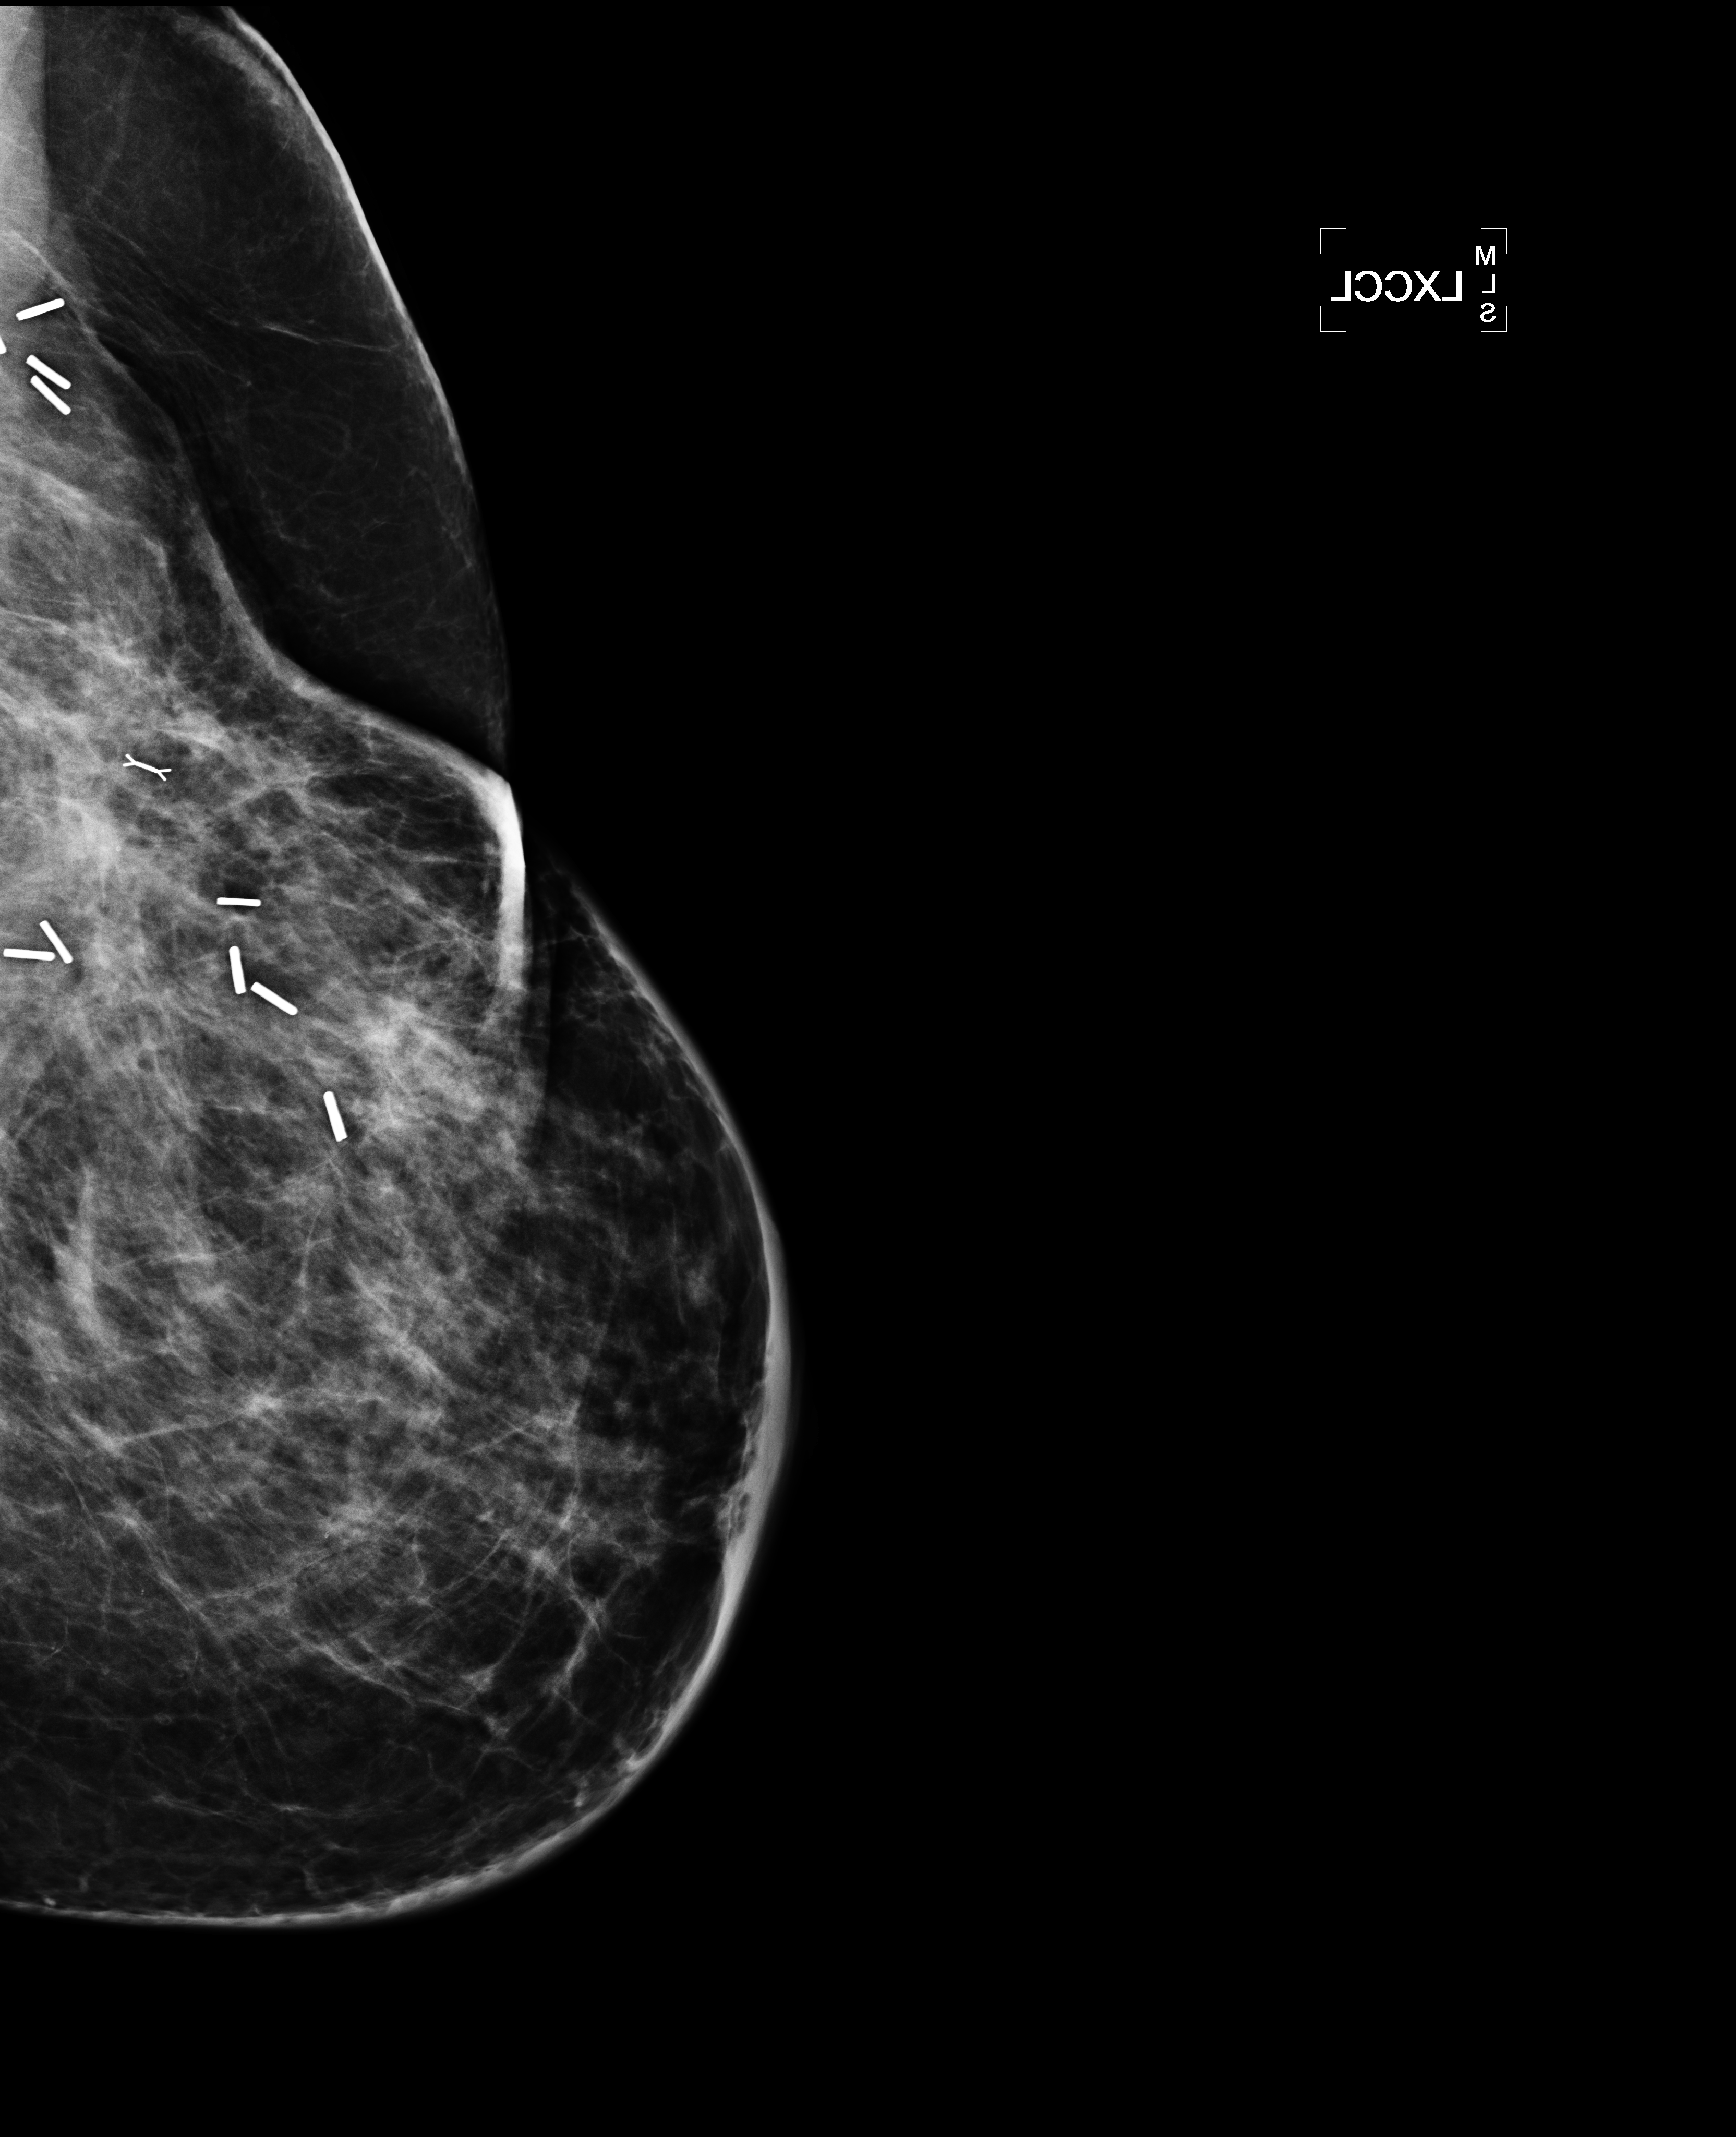
Mammogram, left breast, XCCL view.
Patient-level pathology facts (clinical record, not image findings): pathology diagnosis: Invasive ductal CA (left breast); receptor status (as recorded): ER pos, PR pos (weak), HER2 neg; Ki-67 (as recorded): intermed prolif; pathology report notes: re-bx [date] was scar tissue from RT rx.